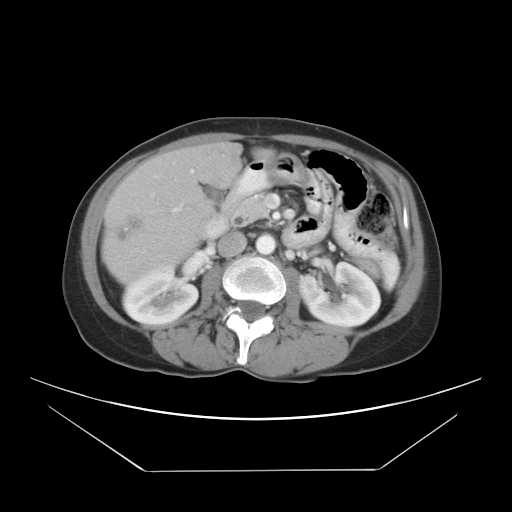
Contrast-enhanced abdominal CT, one axial slice. Reconstruction kernel STANDARD. Intravenous contrast given. Soft-tissue window (W 400 / L 40 HU). 7.5 mm slice thickness. 512 × 512 image matrix, field of view 412 × 412 mm. Female patient, age 54 years. Case-level facts recorded for this patient, not image findings: diagnosis: colorectal cancer liver metastases, imaged before liver resection; multiple liver metastases: yes; largest metastasis: 2.5 cm.
Annotated regions visible in this slice (expert manual segmentation):
- liver: bounding box <106,145,240,281> (left, top, right, bottom; pixels)
- planned liver remnant (the part of the liver to remain after resection): <119,145,240,260>
- portal vein (with intrahepatic branches): <173,168,195,212>
- liver metastasis: <116,217,145,244>